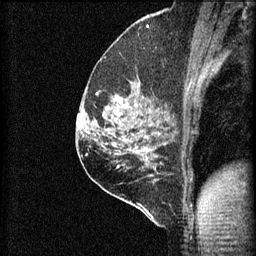
Breast MRI (dynamic contrast-enhanced), one sagittal slice; slice 40 of 60 in the series (ordered by position); 3 images stored at this slice position (order not interpretable as contrast timing); 1.5 T; TE 4.2 ms, TR 8.2 ms; 2 mm slice thickness; 256 × 256 image matrix, field of view 180 × 180 mm. Patient: female, 59 years.
Outlined on this slice (semi-automatic segmentation, software-assisted and operator-edited):
- analysis volume of interest (the breast-tissue region the enhancement analysis was run in; not a lesion): bounding box <92,74,155,131> (left, top, right, bottom; pixels)
- tumour enhancement mask (voxels above the 70 % enhancement threshold inside the analysis volume of interest): <106,96,120,115>